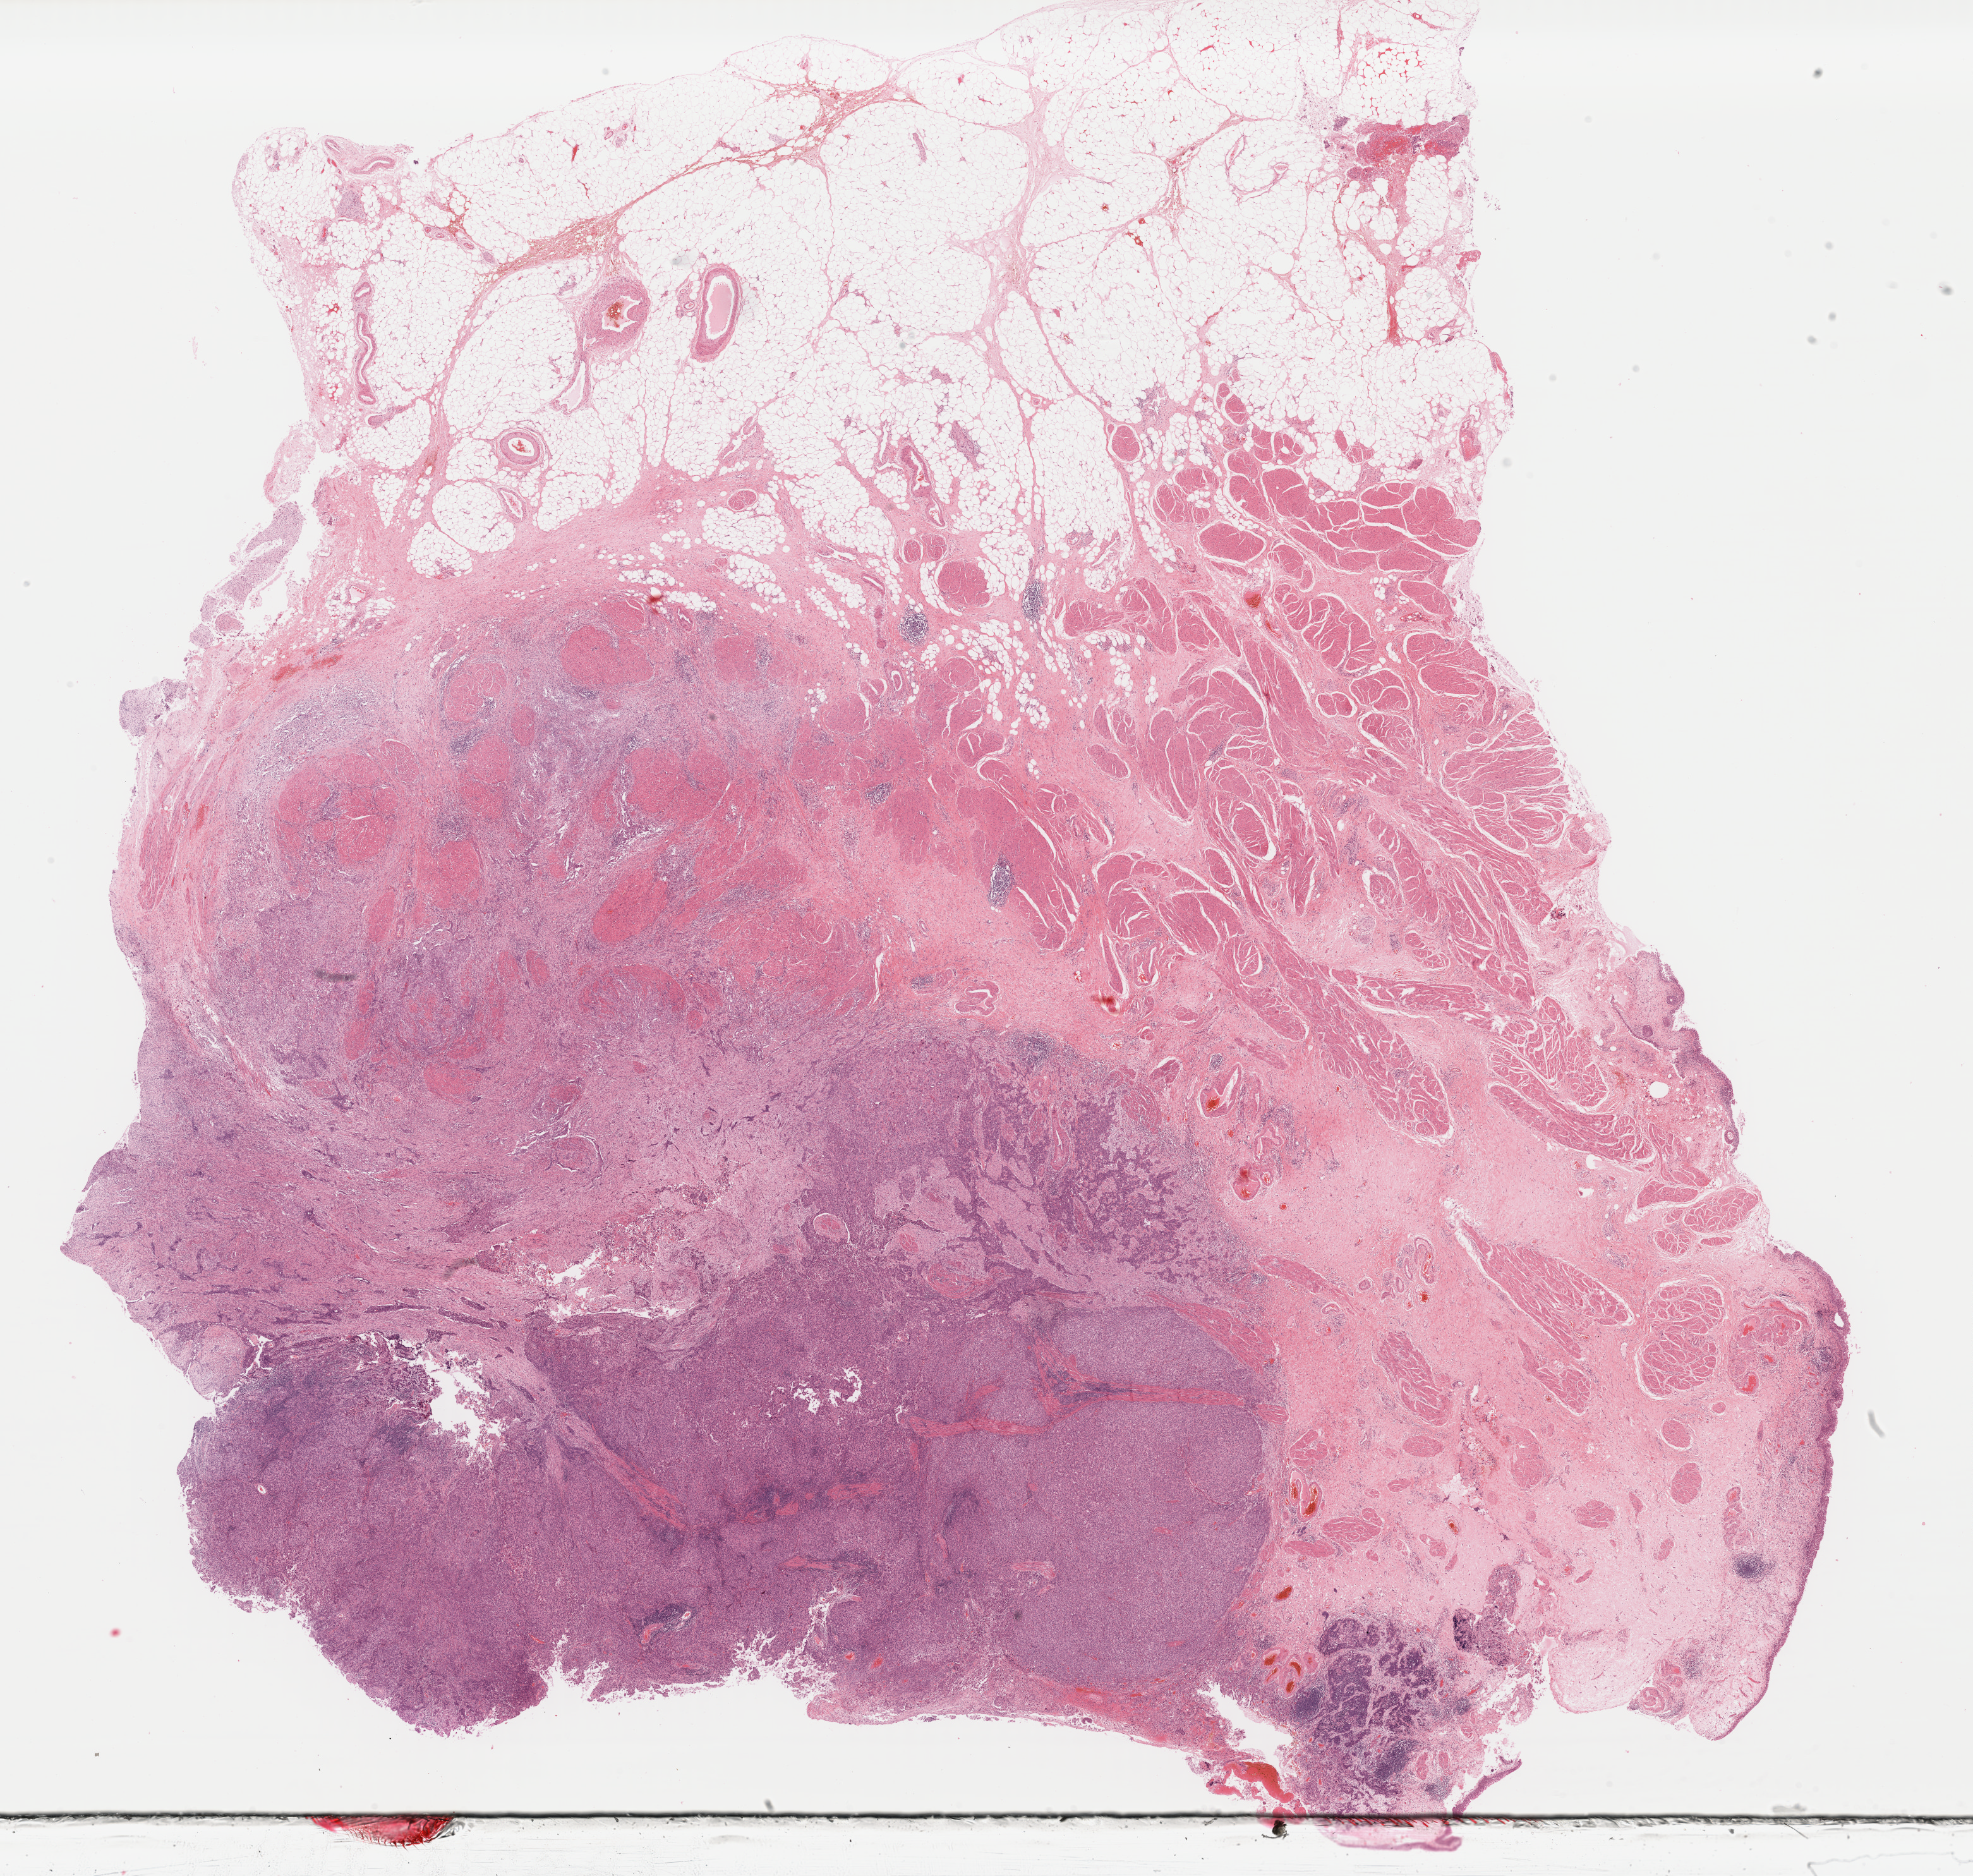
Whole-slide histology image, H&E, shown as a low-resolution overview of the whole scanned area (about 24.6 x 23.4 mm, from a 40x scan), formalin-fixed paraffin-embedded (FFPE) diagnostic section, sample: primary tumour, bladder. Patient: male, age at initial diagnosis 75 years. Histologic grade: high grade.
Diagnosis: Transitional cell carcinoma (anterior wall of bladder). AJCC pathologic stage: II (7th edition).